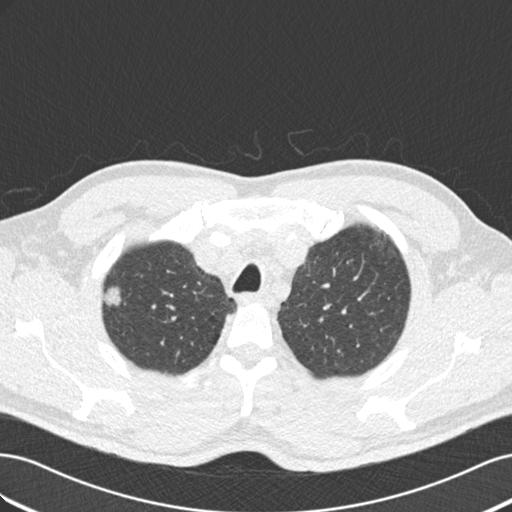
Low-dose screening chest CT, axial slice. Second annual screen. Lung window (W 1500 / L -600 HU). Slice 38 of 187 in the series. 512 × 512 image matrix, field of view 360 × 360 mm. Male participant, aged 56 years at enrolment. Current smoker at enrolment.
Expert reader's lesion annotation, bounding box [x1, y1, x2, y2] px = [90, 280, 133, 315]. The exam's reader record, not a measurement of the box and not confirmed to be the same lesion: non-calcified nodule or mass ≥4 mm, right upper lobe, 13 × 12 mm, smooth margins, mixed attenuation, pre-existing on the prior screen: yes; interval growth: yes.